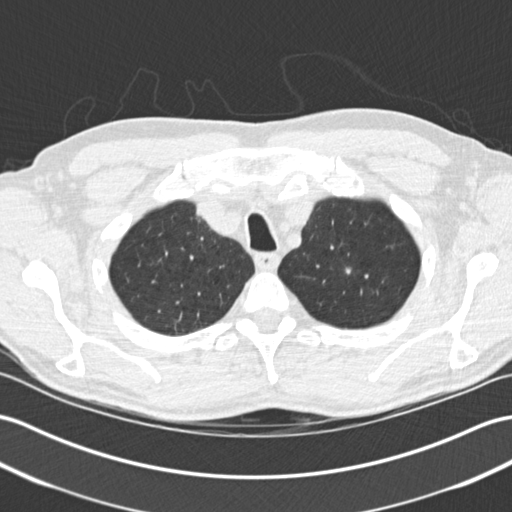
Axial slice from a low-dose chest CT screening exam, baseline screening round, lung window (W 1500 / L -600 HU), 2 mm slice thickness, standard (soft-tissue) reconstruction kernel (B30f), slice 37 of 205 in the series, 512 × 512 image matrix, field of view 353 × 353 mm. Male, age 64 years at enrolment.
- Lesion marked by an expert reader, bounding box (x1, y1, x2, y2) in pixels: (330, 258, 363, 288).
- Reader record for this screening exam (exam-level; its link to the box is not recorded): non-calcified nodule or mass ≥4 mm, right upper lobe, 7 × 5 mm, spiculated (stellate) margins, soft tissue attenuation.
- Note: the box lies in the patient's left hemithorax on this image, whereas the reader's record names the right lung; they may be different findings.
- Later outcome: lung cancer diagnosed 833 days after this screen — adenocarcinoma, NOS, left upper lobe, poorly differentiated (G3), stage IA (AJCC 6th edition), 10 mm at pathology.